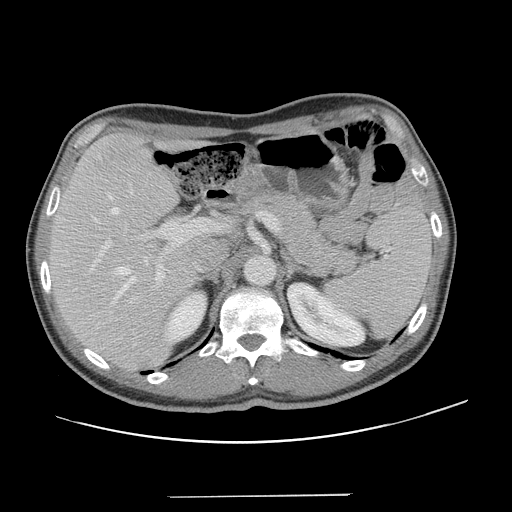
Contrast-enhanced abdominal CT, one axial slice; 120 kVp; soft-tissue window (W 400 / L 40 HU); 512 × 512 image matrix, field of view 403 × 403 mm. Male patient, age 60 years. From the clinical record (not read from this slice): diagnosis: colorectal cancer liver metastases, imaged before liver resection; multiple liver metastases: no; largest metastasis: 2.5 cm; disease in both lobes: no.
Structures marked on this image (expert manual segmentation):
- hepatic veins: bounding box (x1, y1, x2, y2) in pixels: (108, 193, 147, 304)
- liver: (50, 133, 196, 369)
- planned liver remnant (the part of the liver to remain after resection): (50, 133, 197, 355)
- portal vein (with intrahepatic branches): (96, 218, 229, 288)